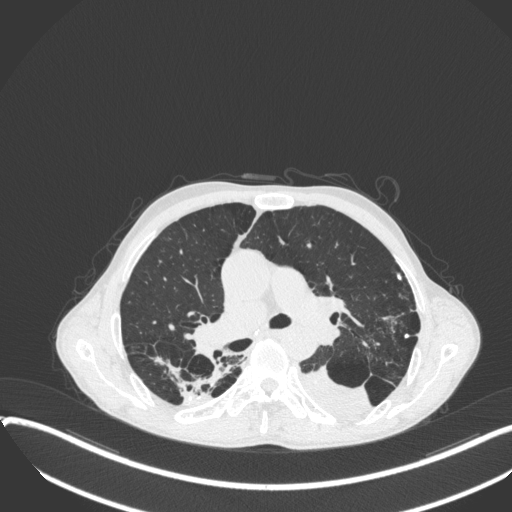
Chest CT, one axial slice; position 236 of 400 along the scan axis; 120 kVp; lung window (W 1500 / L -600 HU); 512 × 512 image matrix, field of view 400 × 400 mm. Male patient, age 57 years. From the clinical record (not read from this slice): clinical TNM (as recorded): T4 N0 M0.
Structures marked on this image (rectangle marked by the reading radiologist):
- lung tumour (recorded histology: squamous cell carcinoma): bounding box (x1, y1, x2, y2) in pixels: (297, 361, 376, 420)